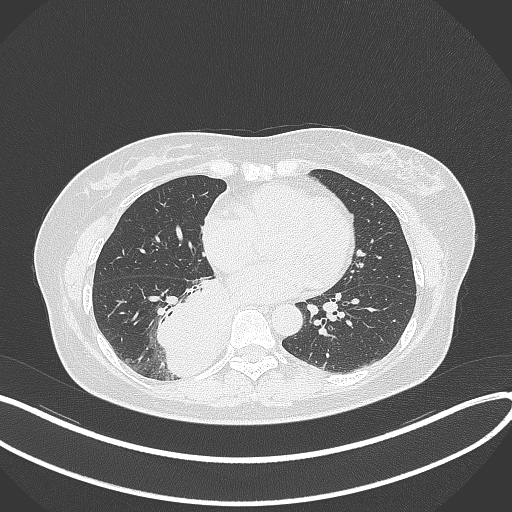
Chest CT, one axial slice. Position 145 of 331 along the scan axis. Reconstruction kernel B70f. 120 kVp. Lung window (W 1500 / L -600 HU). 1 mm slice thickness. 512 × 512 image matrix, field of view 400 × 400 mm. Patient: female, 54 years. Case-level facts recorded for this patient, not image findings: clinical TNM (as recorded): T4 N0 M0.
Structures marked on this image (bounding box drawn by a radiologist):
- lung tumour (recorded histology: adenocarcinoma): box from (x=154, y=278) to (x=233, y=382) px